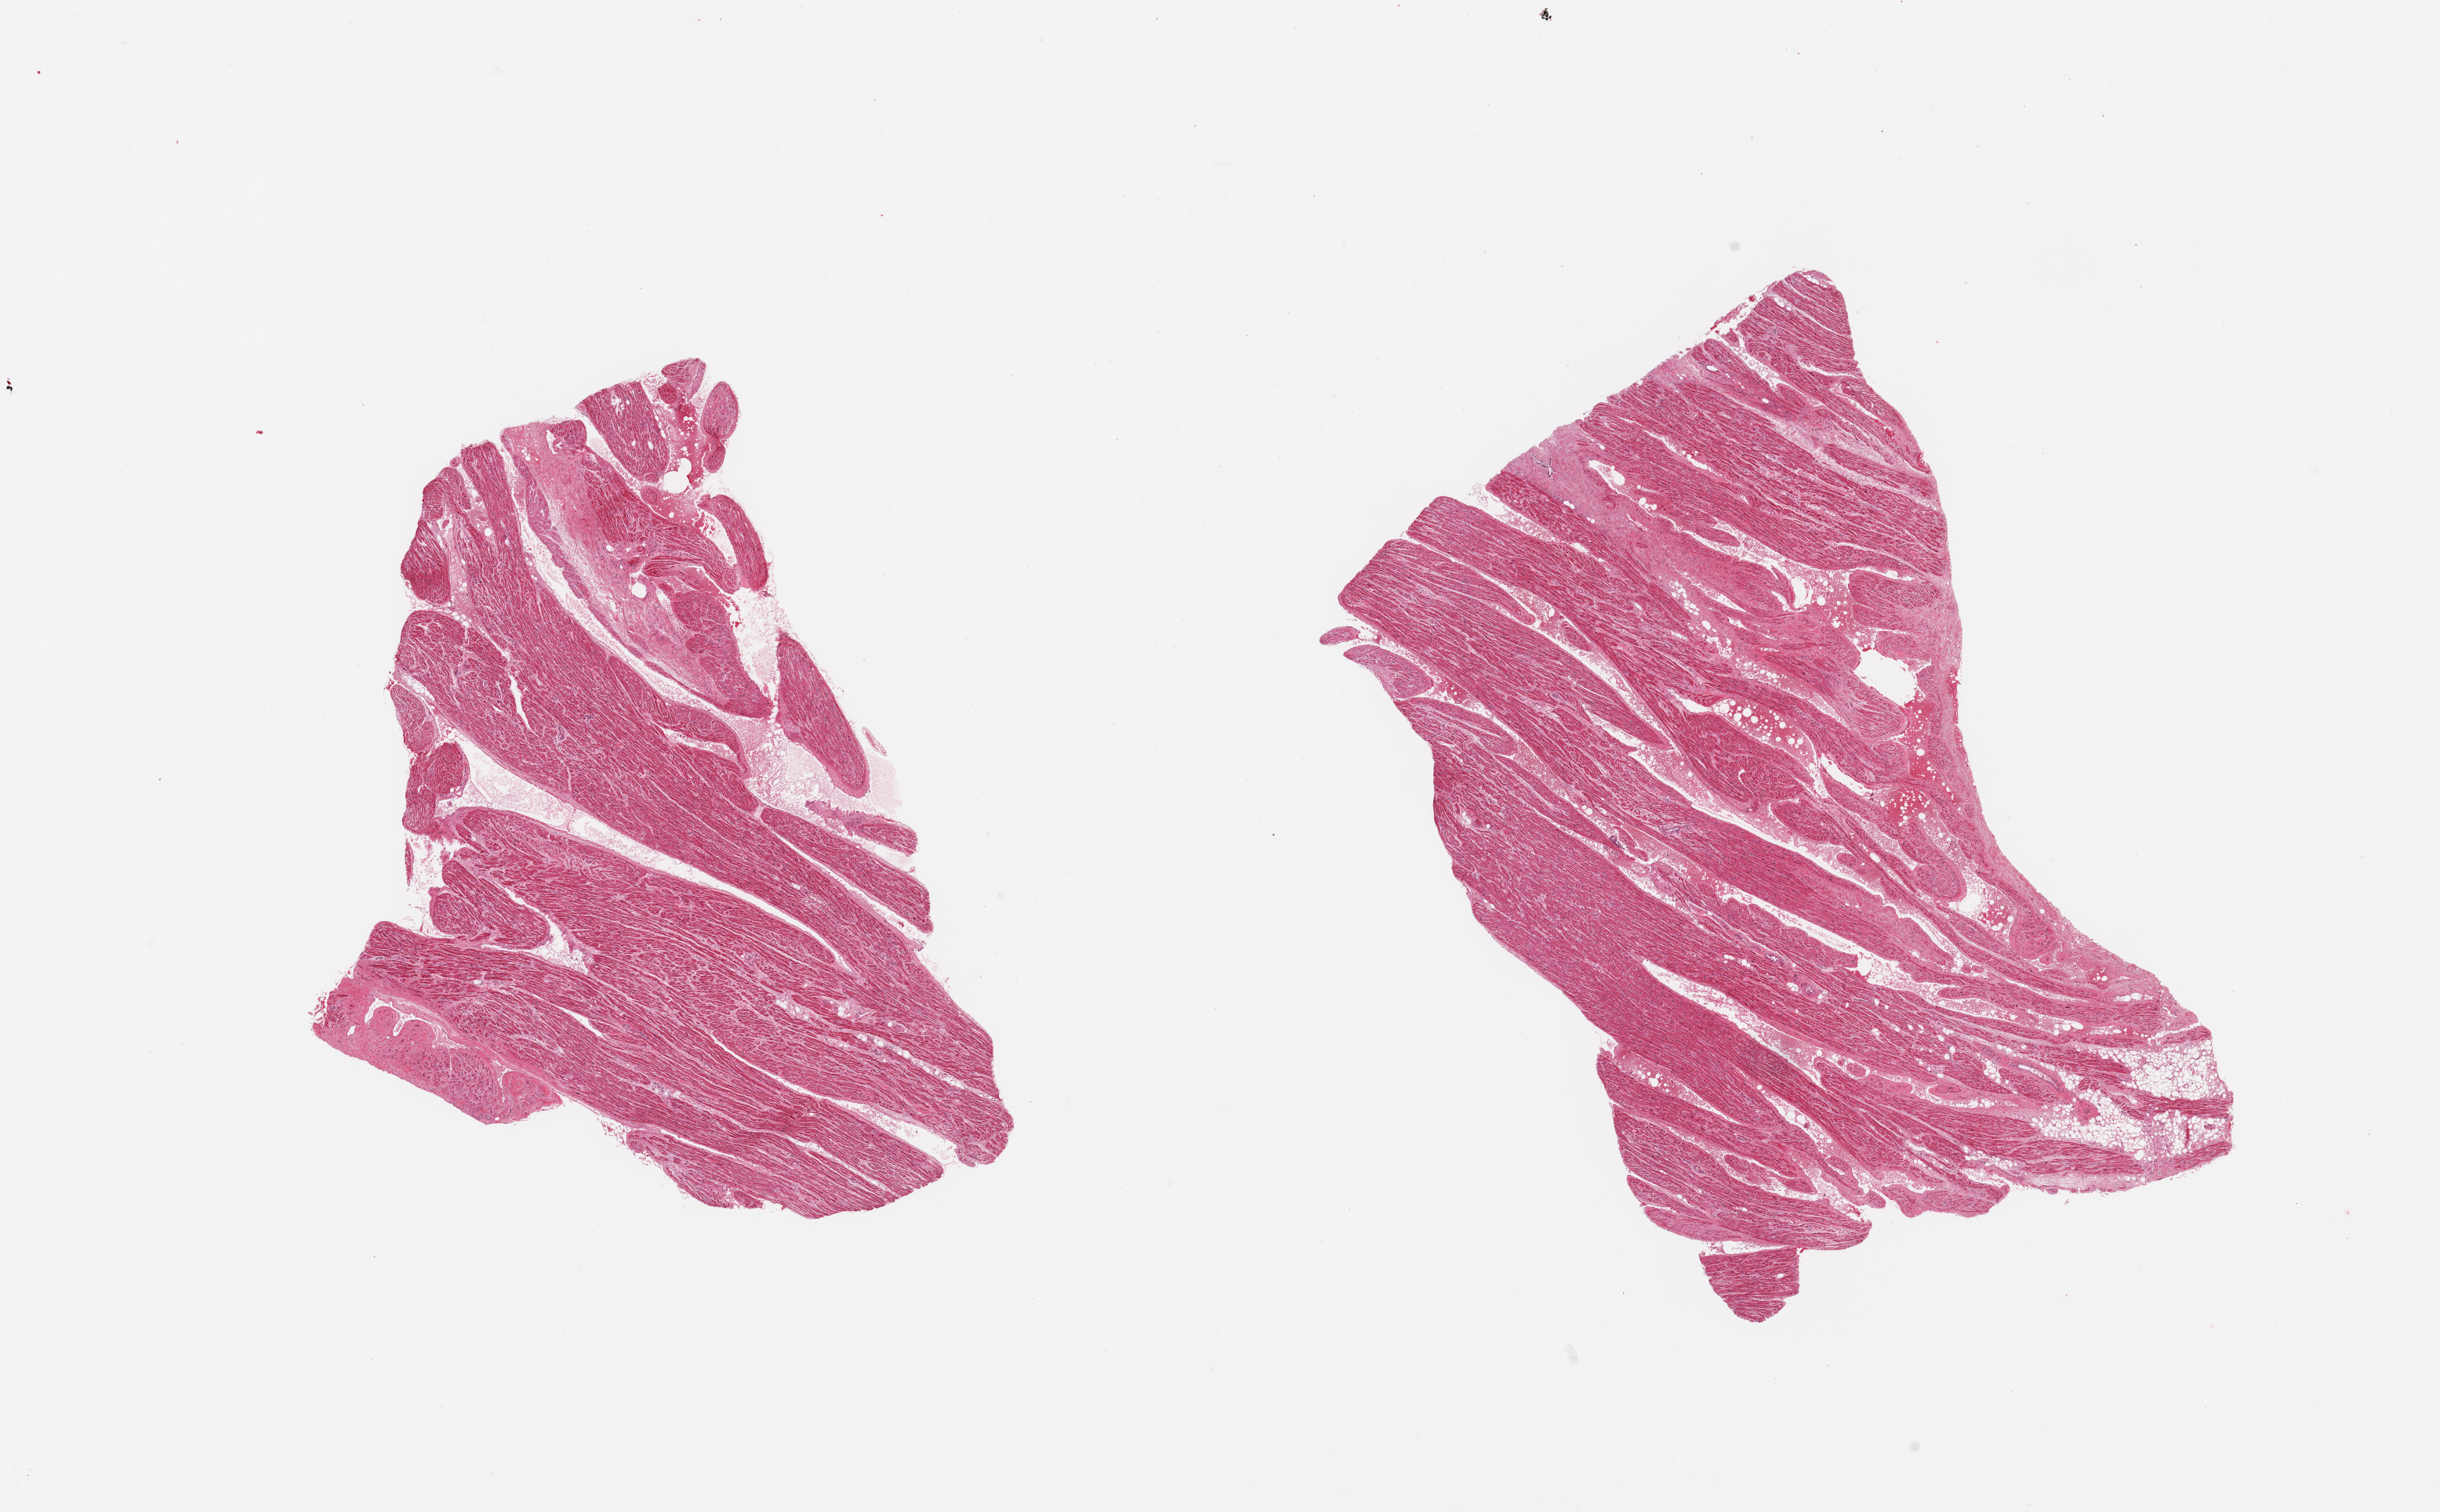
Digitized hematoxylin and eosin (H&E)-stained section, low-resolution overview of the scanned area, about 24.6 x 15.3 mm (from a 20x scan), PAXgene-fixed paraffin-embedded (PFPE) section, sampled site (target tissue): auricular appendage, tissue donor sample. Donor sex: male.
Reviewer comment on this tissue sample: 2 pieces; ~ 10% of internal fat.